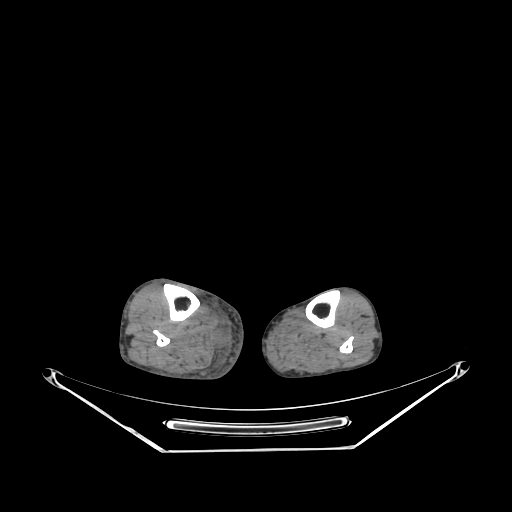
CT of an extremity soft-tissue mass (from a PET/CT study), one axial slice. Position 121 of 267 along the scan axis. 140 kVp. Soft-tissue window (W 400 / L 40 HU). 3.75 mm slice thickness. 512 × 512 image matrix, field of view 500 × 500 mm. Male patient. From the clinical record (not read from this slice): histological type: pleiomorphic liposarcoma; grade: high; site of the primary tumour: right calf.
Outlined on this slice (expert contour drawn on MRI and transferred to this co-registered scan by the dataset authors):
- gross tumour volume including surrounding oedema: bounding box <212,335,222,346> (left, top, right, bottom; pixels)